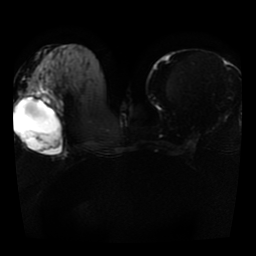
Breast MRI, one axial slice. Position 16 of 41 along the scan axis. Diffusion-weighted series; image 2 of 4 stored at this slice position (different b-values; order by instance number). 1.5 T. 256 × 256 image matrix, field of view 330 × 330 mm. Female patient.
Outlined on this slice (expert manual segmentation):
- tumour on diffusion-weighted imaging: bounding box (x1, y1, x2, y2) in pixels: (51, 99, 61, 107)